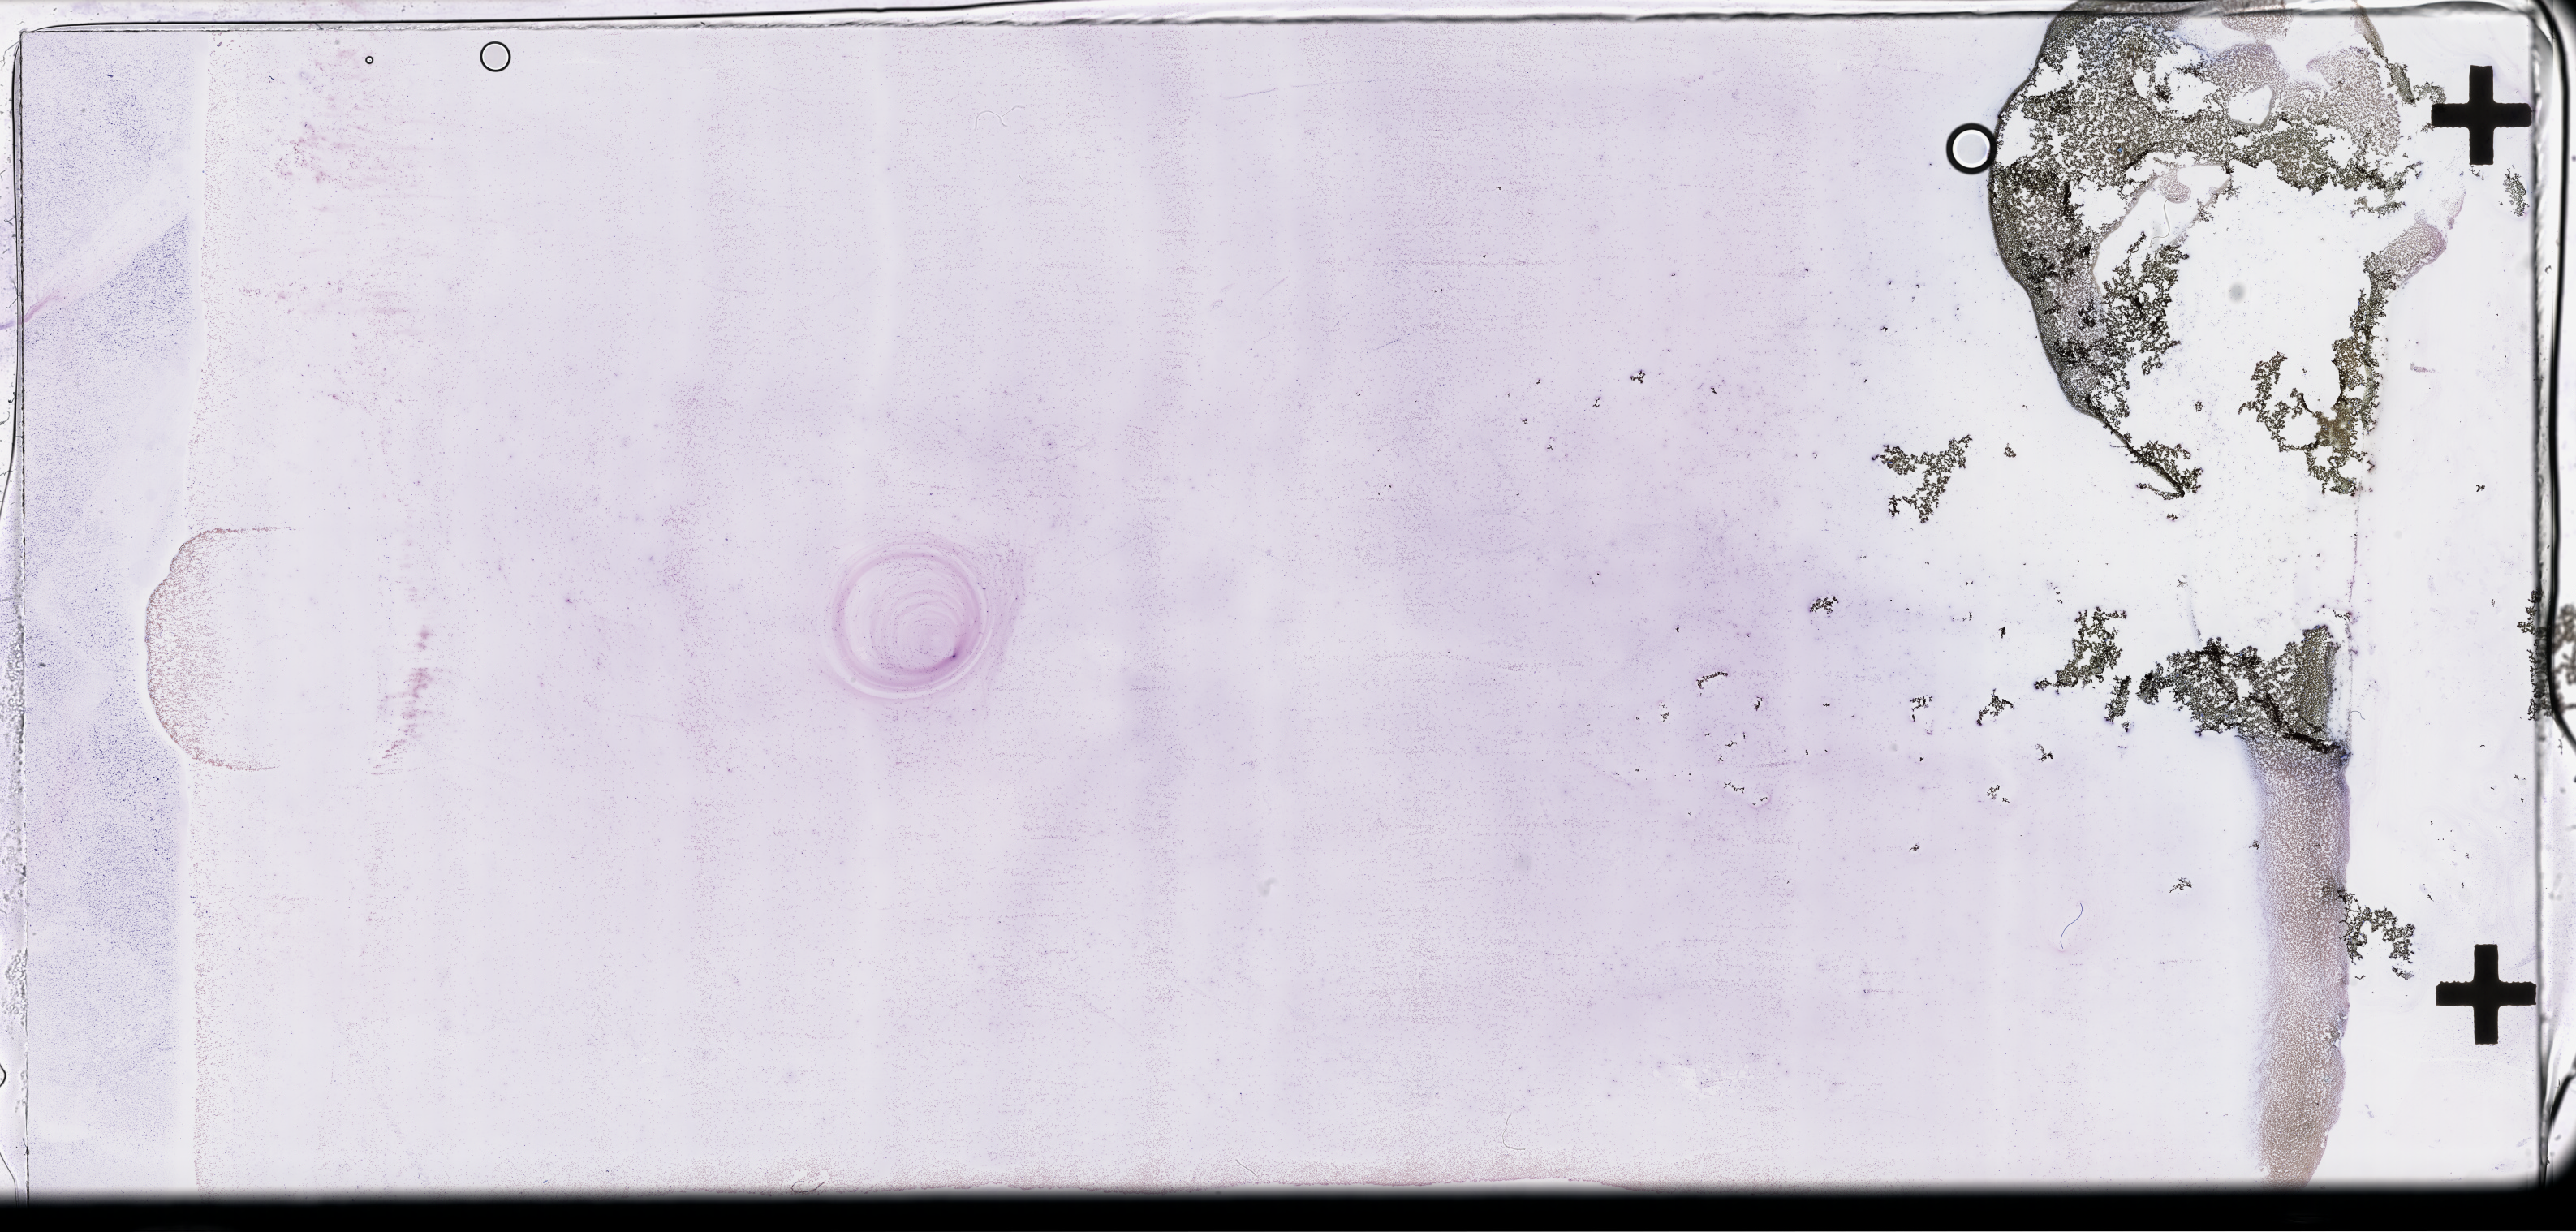
Wright–Giemsa-stained whole blood smear, whole-slide image, shown as a low-resolution overview of the whole scanned area (about 51.3 x 24.5 mm); EDTA-anticoagulated smear. Male patient.
* patient diagnosis: Plasma Cell Myeloma